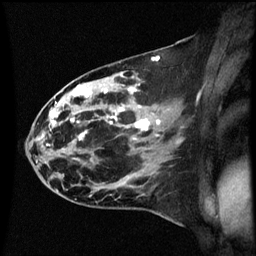
Breast MRI (dynamic contrast-enhanced), one sagittal slice. Position 32 of 60 along the scan axis. Dynamic contrast-enhanced series, image 2 of 3 at this slice position (ordered by acquisition). 1.5 T. TE 4.2 ms, TR 8.9 ms. 2 mm slice thickness. 256 × 256 image matrix, field of view 200 × 200 mm. Patient: female, 44 years. Case-level facts recorded for this patient, not image findings: setting: breast cancer imaged before/during neoadjuvant chemotherapy; receptor status: HR-positive, HER2-negative.
Annotated regions visible in this slice (semi-automatically segmented with operator editing):
- analysis volume of interest (the breast-tissue region the enhancement analysis was run in; not a lesion): bounding box (x1, y1, x2, y2) in pixels: (43, 78, 153, 189)
- tumour enhancement mask (voxels above the 70 % enhancement threshold inside the analysis volume of interest): (50, 86, 150, 139)